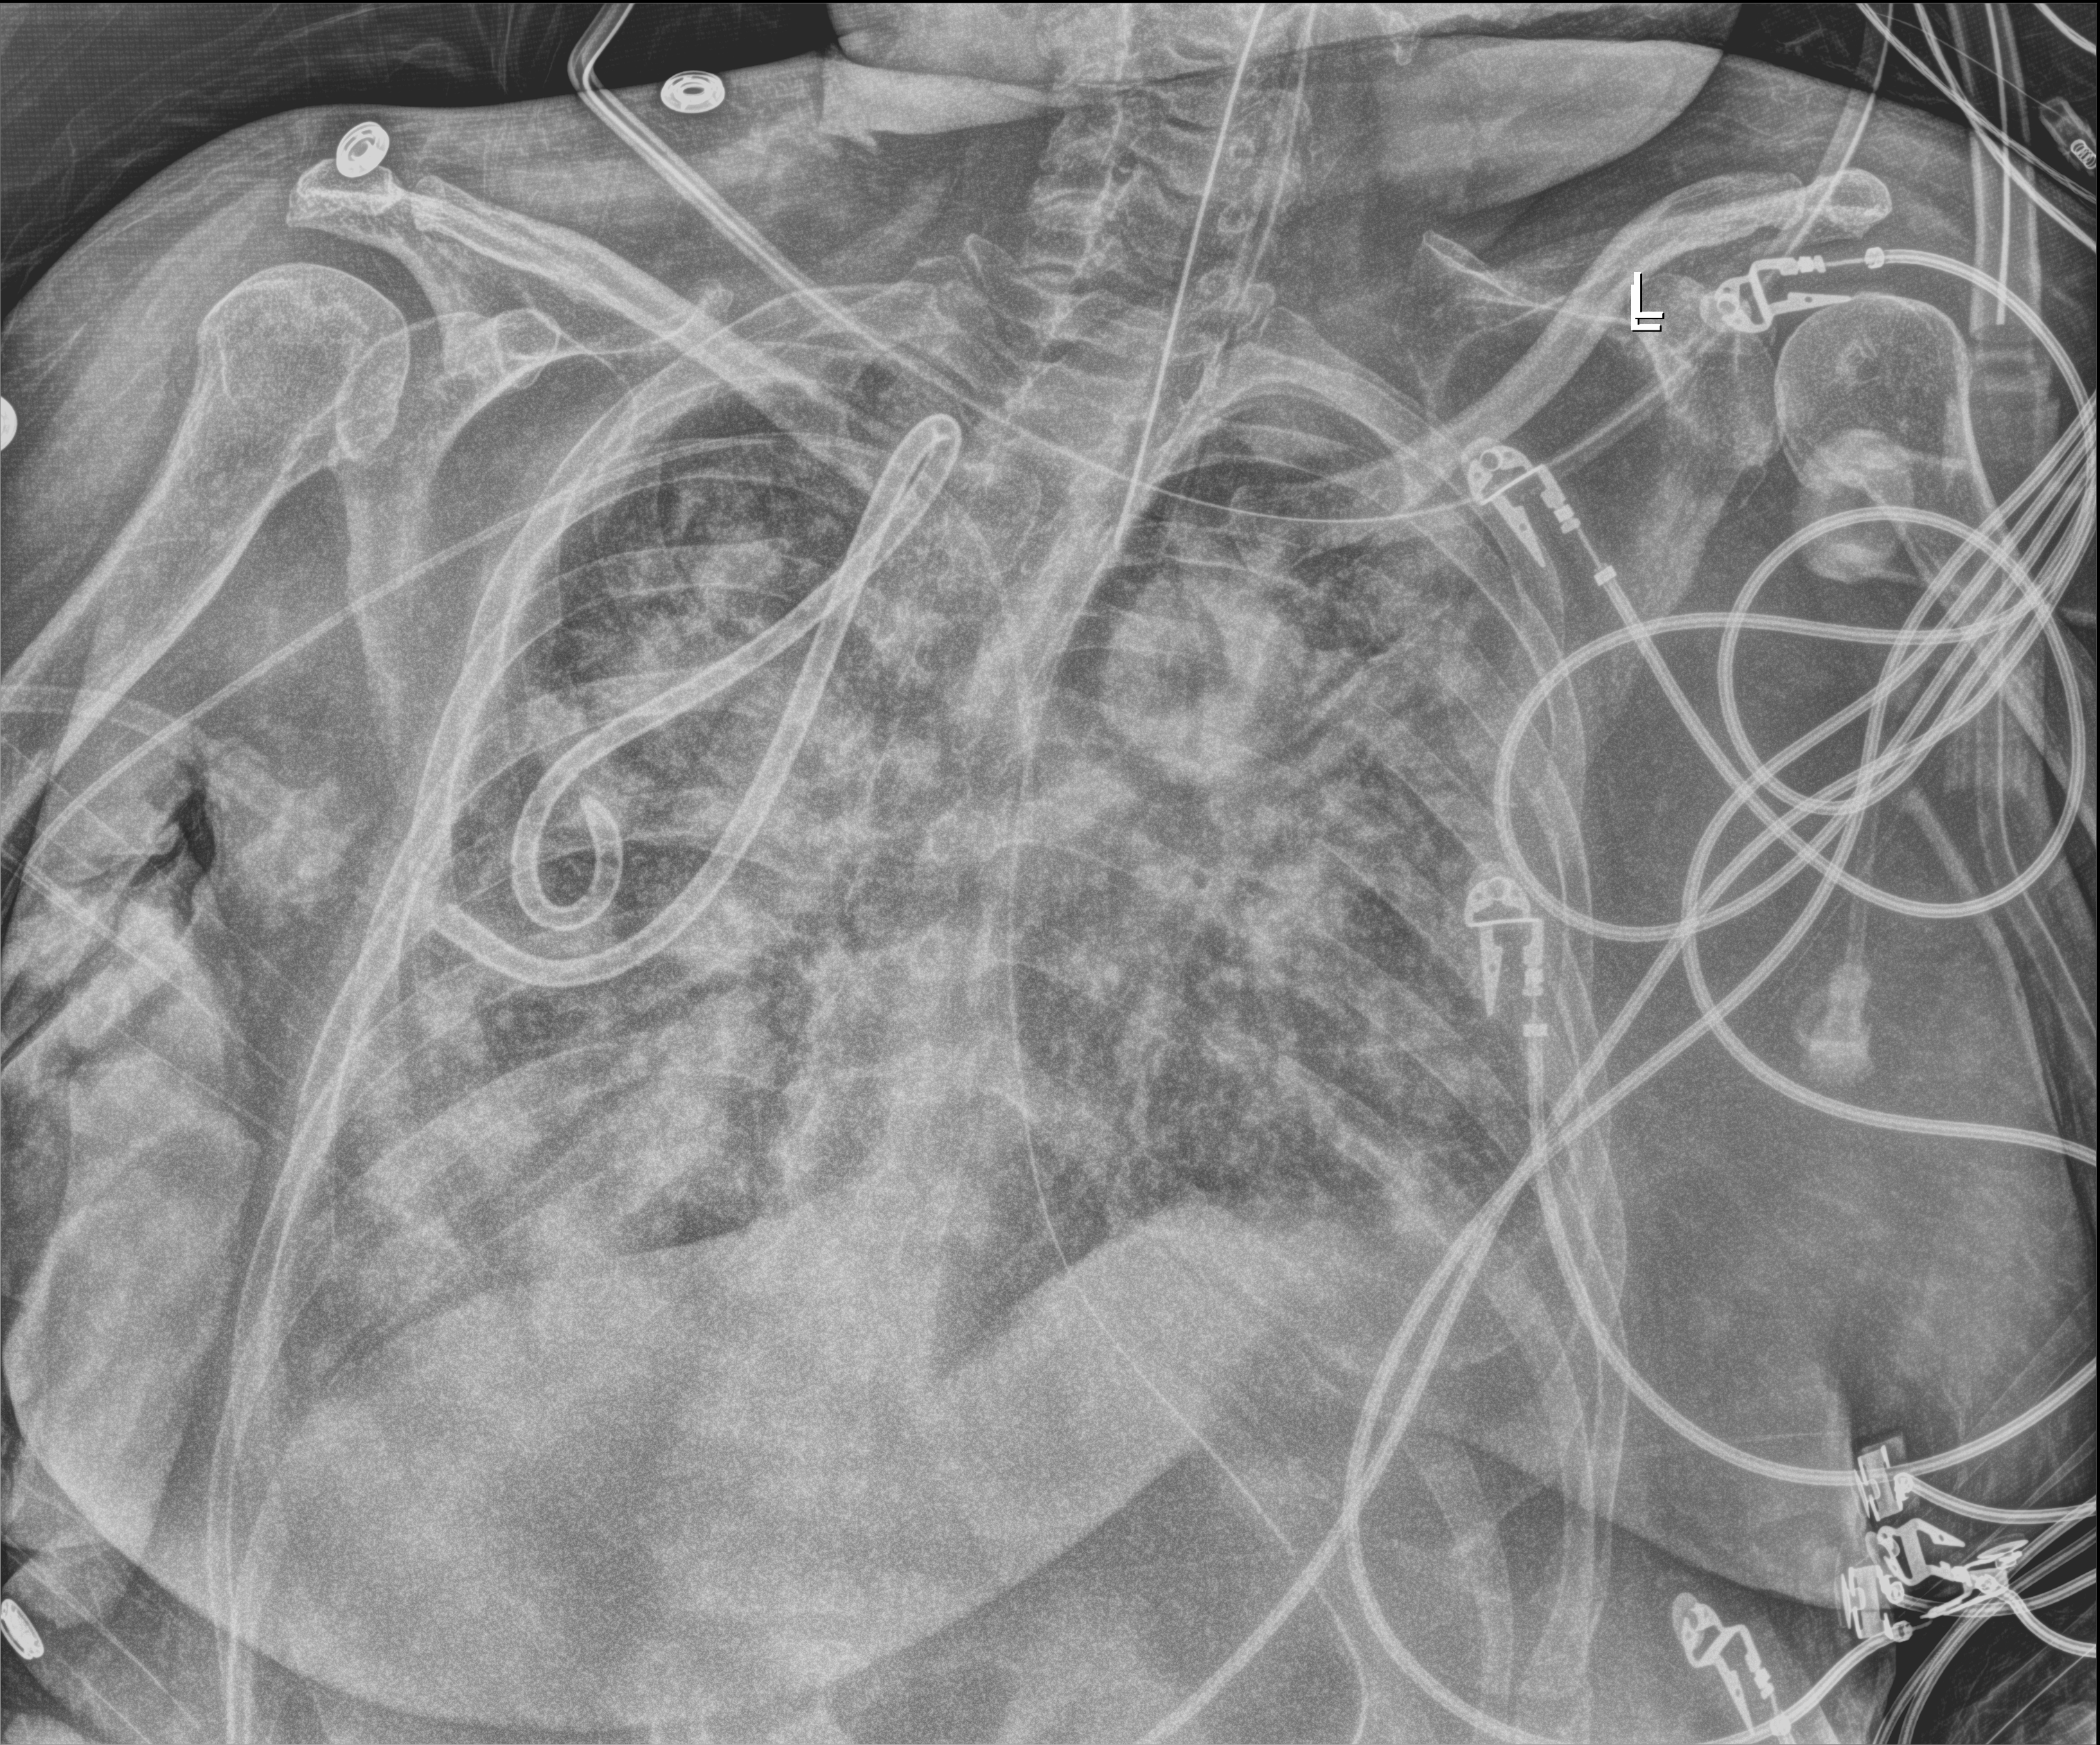
Portable chest radiograph, anteroposterior (AP) projection. Patient hospitalised with COVID-19, aged 18–59 years.
From the hospital-stay record, not from the radiograph (when in the stay this image was taken is not recorded): mechanically ventilated during this hospital stay: yes.